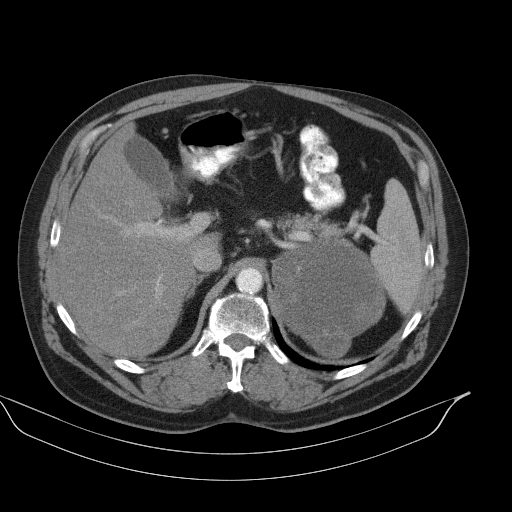
Contrast-enhanced abdominal CT, one axial slice; reconstruction kernel B41s; 130 kVp; intravenous contrast given; soft-tissue window (W 400 / L 40 HU); 5 mm slice thickness; 512 × 512 image matrix. Patient: male, 56 years. Case-level facts recorded for this patient, not image findings: diagnosis: adrenocortical carcinoma; tumour side: left adrenal; tumour size at pathology: 15 cm; Ki-67 index: 35 %; stage (as recorded): 4.
Outlined on this slice (semi-automatic segmentation, software-assisted and operator-edited):
- mass: bounding box (x1, y1, x2, y2) in pixels: (274, 238, 385, 357)